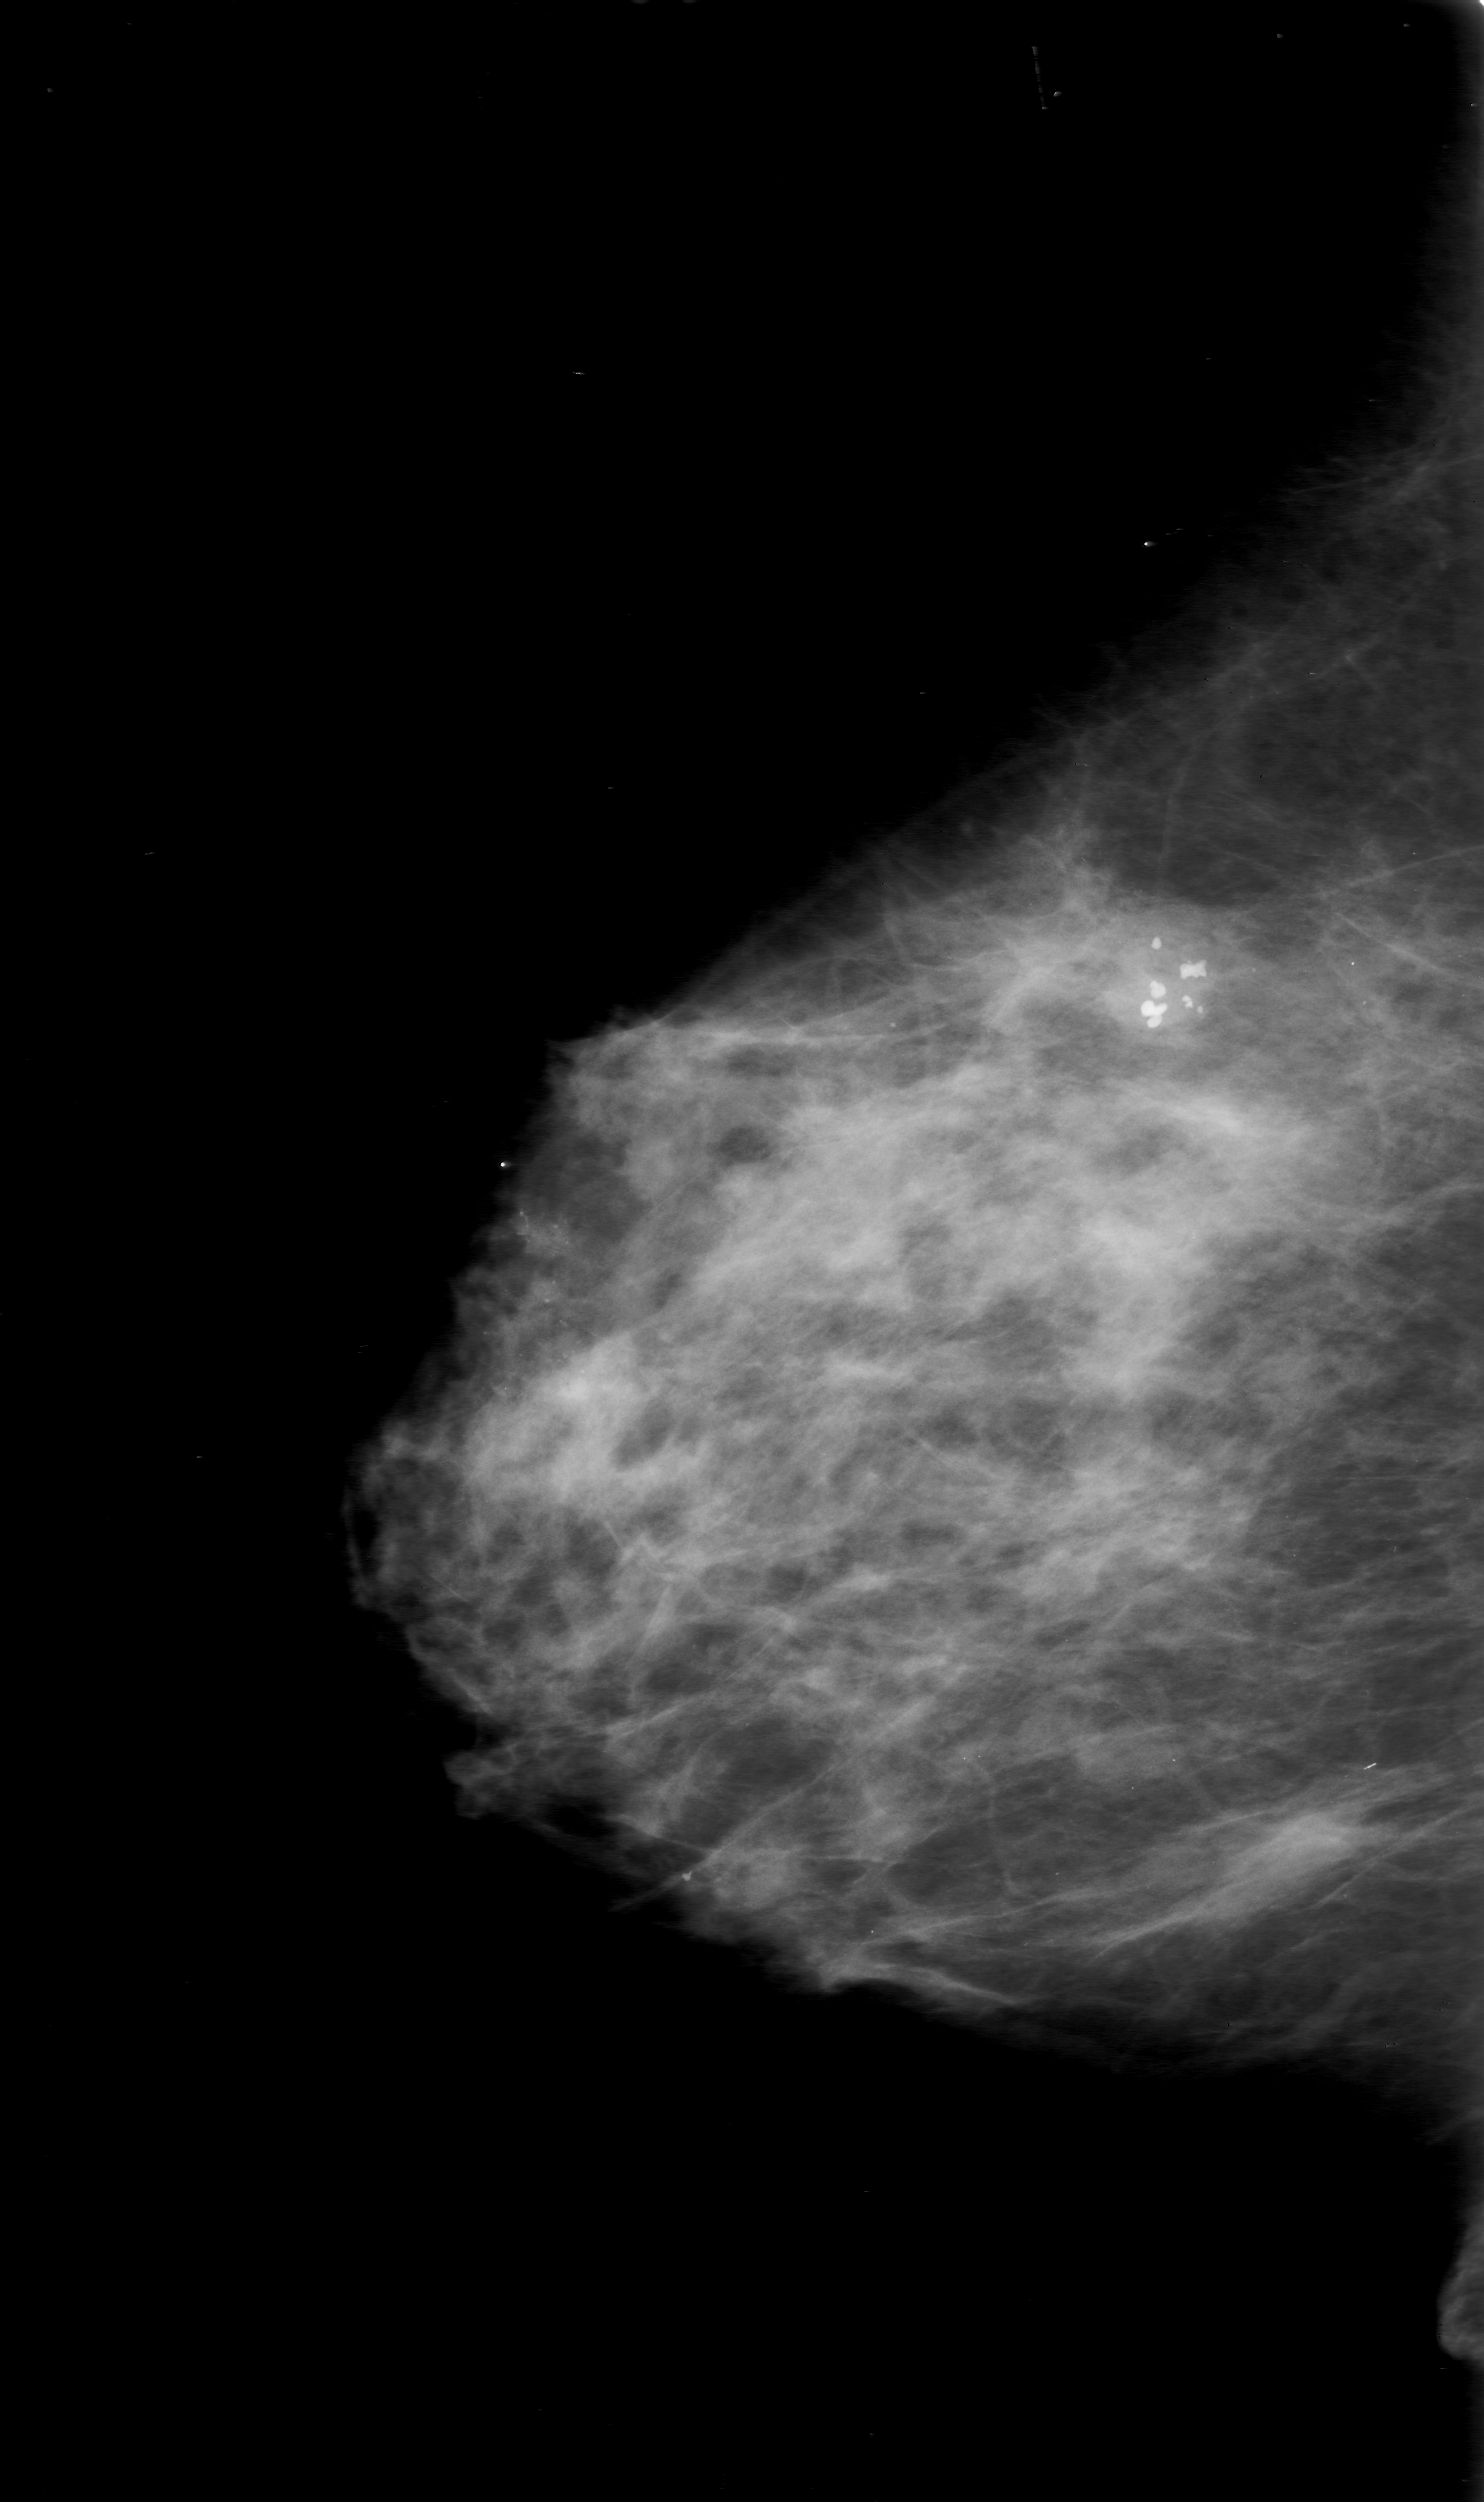
Mammogram (digitized film); right breast; mediolateral oblique (MLO) view; breast composition: heterogeneously dense (BI-RADS density category 3 of 4); 1484 × 2502 image matrix.
Marked abnormalities (boxes around the expert regions of interest):
- calcifications, morphology punctate / fine linear branching, distribution clustered; BI-RADS assessment category 0 (incomplete: needs additional imaging); subtlety rating 5 on a 1 (subtle) to 5 (obvious) scale; pathology result (as recorded, not read from the image): malignant: bounding box [x1, y1, x2, y2] px = [396, 1106, 688, 1462]